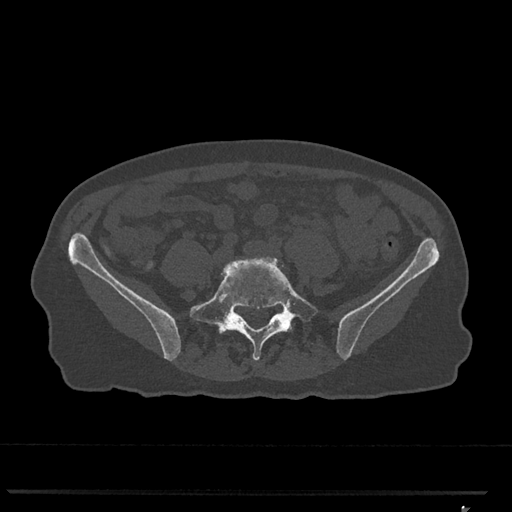
CT including the spine, one axial slice; position 154 of 793 along the scan axis; reconstruction kernel Br40s/3; bone window (W 1800 / L 400 HU); 0.5 mm slice thickness; 512 × 512 image matrix. Female patient, age 62 years. From the clinical record (not read from this slice): primary cancer: renal.
Structures marked on this image (semi-automatic segmentation, software-assisted and operator-edited):
- L4 vertebra: bounding box (x1, y1, x2, y2) in pixels: (247, 259, 251, 260)
- L5 vertebra: (190, 257, 318, 360)